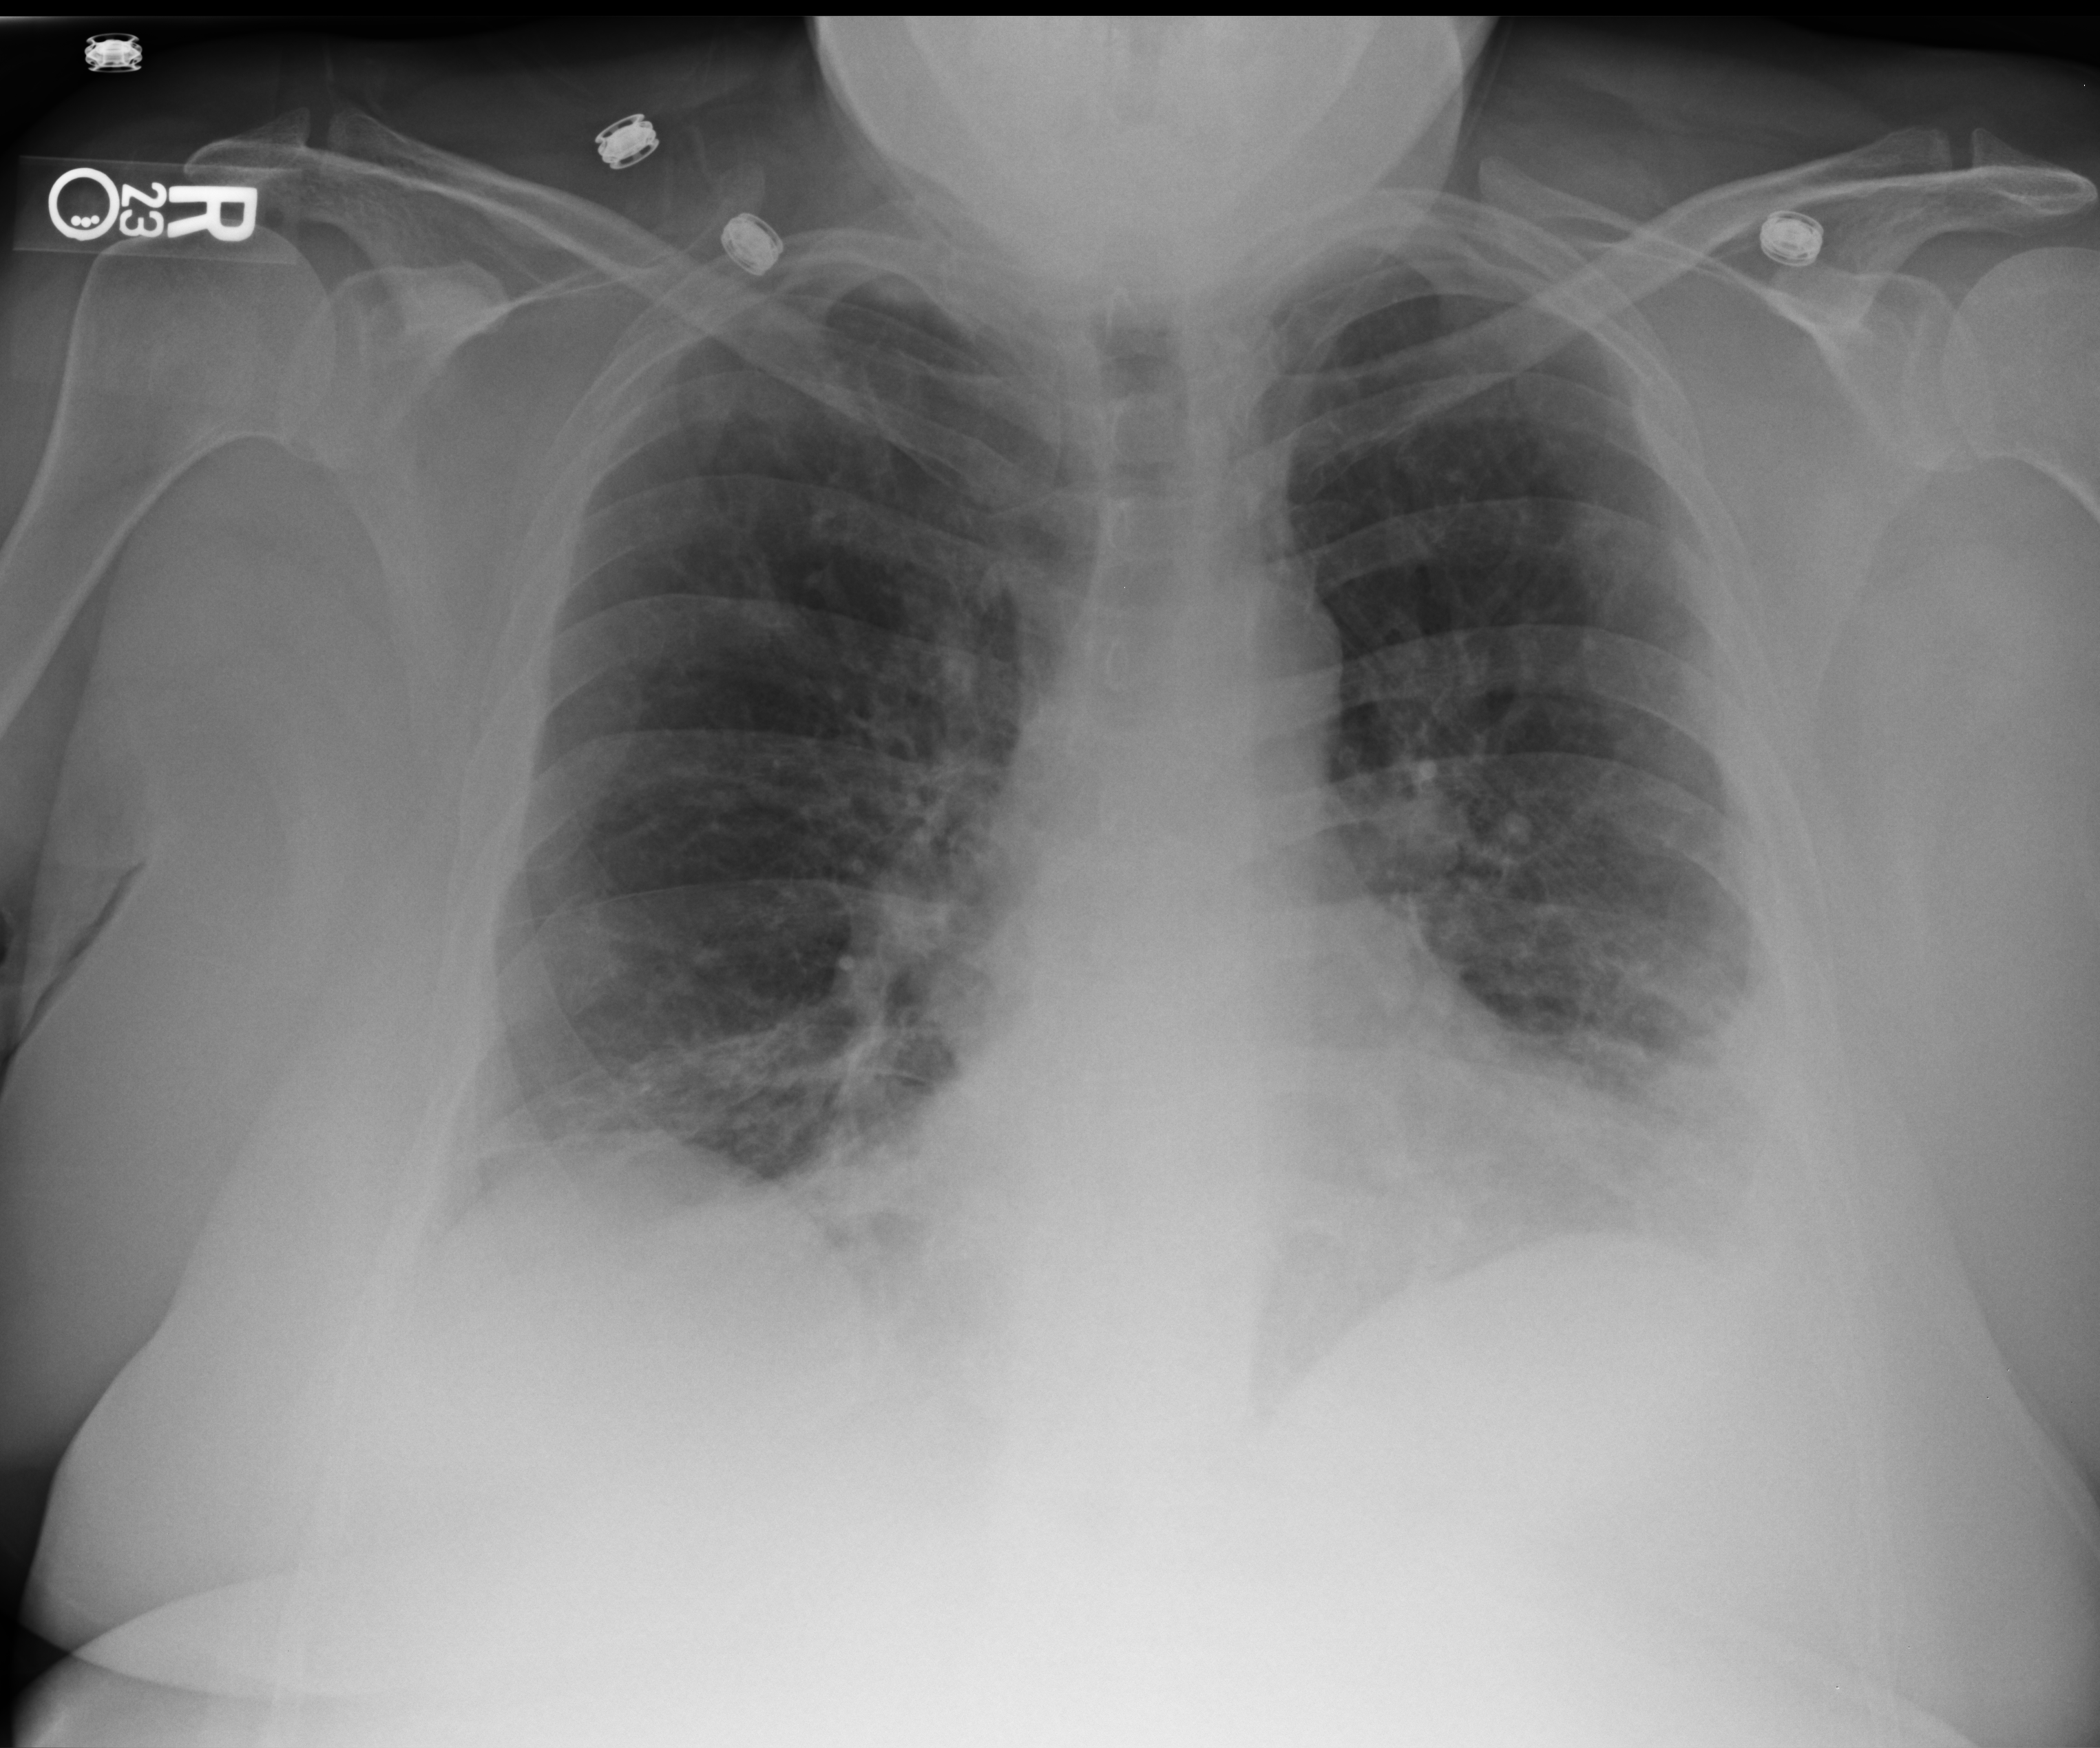
Portable chest radiograph; anteroposterior (AP) projection. Female patient hospitalised with COVID-19, age 18–59 years.
From the hospital-stay record, not from the radiograph (when in the stay this image was taken is not recorded): length of hospital stay: 10 days.